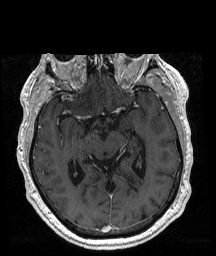
Brain MRI from a brain-tumour surgery series, one axial slice; position 112 of 192 along the scan axis; T1-weighted post-contrast; 216 × 256 image matrix, field of view 211 × 250 mm. Case-level facts recorded for this patient, not image findings: histopathology: Glioblastoma; WHO grade: 4; IDH mutation: no; tumour location: Right Frontal.
Structures marked on this image (manually delineated by an expert):
- tumour: bounding box [x1, y1, x2, y2] px = [58, 92, 67, 99]